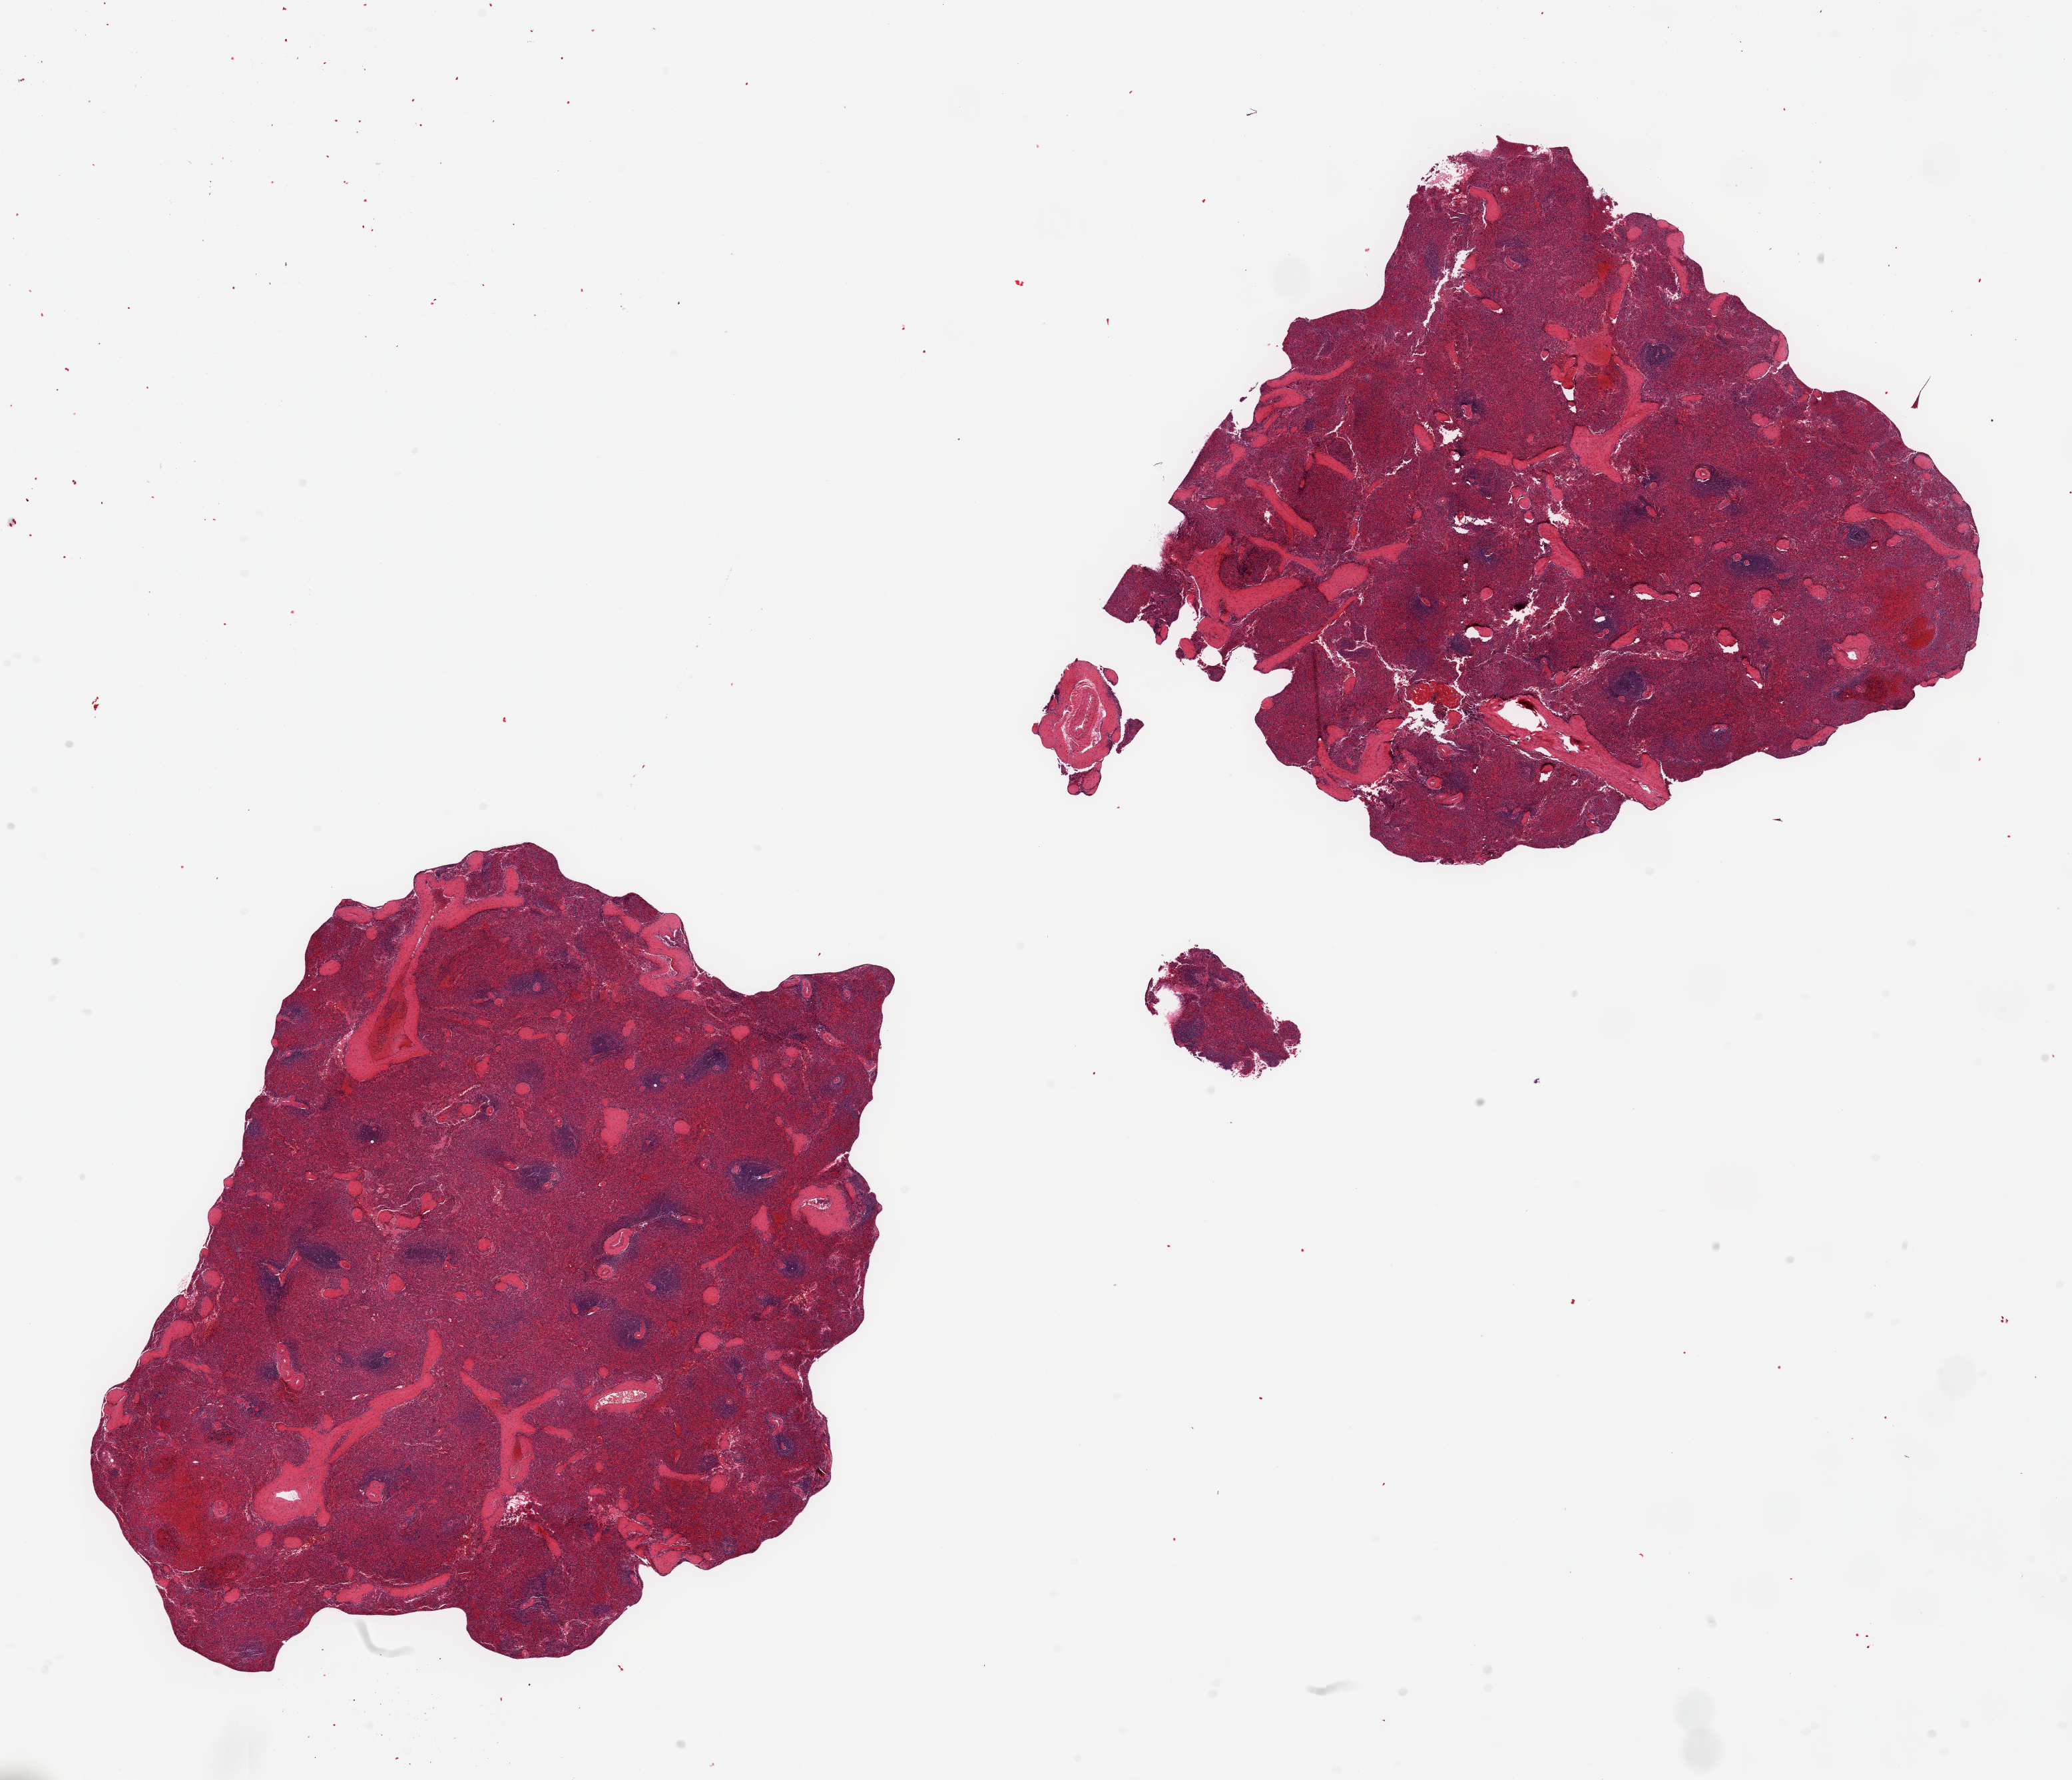
Hematoxylin and eosin (H&E) whole-slide image, brightfield, shown as a low-resolution overview of the whole scanned area (about 24.6 x 21.1 mm, from a 20x scan); PAXgene-fixed, paraffin-embedded tissue; target tissue: spleen; tissue donor sample. Donor sex: male.
- reviewer comment on this tissue sample: 2 pieces, no abnormalities